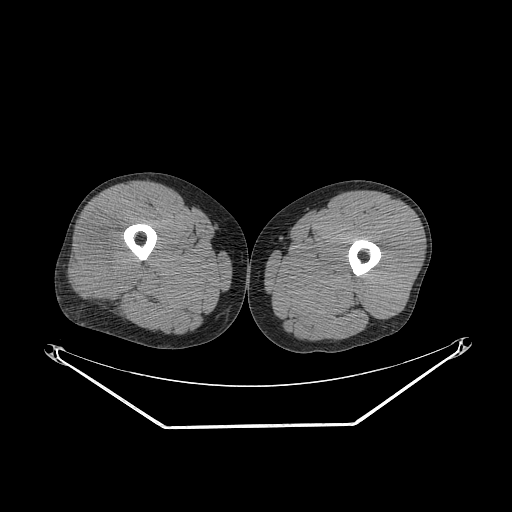
CT of an extremity soft-tissue mass (from a PET/CT study), one axial slice. Slice 242 of 267 in the series (ordered by position). 140 kVp. Soft-tissue window (W 400 / L 40 HU). 512 × 512 image matrix. Male patient. Case-level facts recorded for this patient, not image findings: histological type: poorly differentiated synovial sarcoma; grade: high; site of the primary tumour: right buttock.
Outlined on this slice (expert contour drawn on MRI and transferred to this co-registered scan by the dataset authors):
- gross tumour volume including surrounding oedema: bounding box [x1, y1, x2, y2] px = [73, 224, 136, 303]
- gross tumour volume (mass): [73, 224, 136, 303]